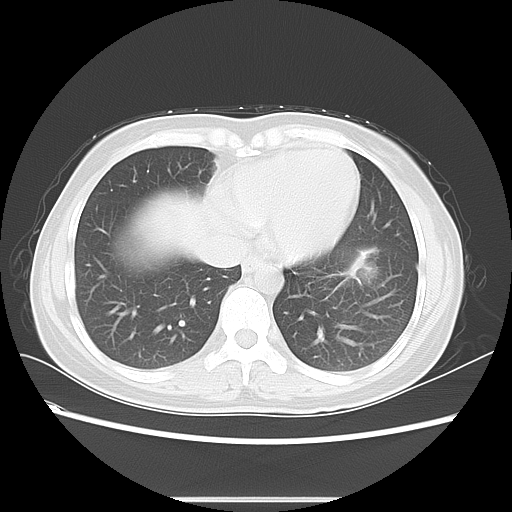
Chest CT, one axial slice; position 20 of 55 along the scan axis; reconstruction kernel LUNG; lung window (W 1500 / L -600 HU); 5 mm slice thickness; 512 × 512 image matrix, field of view 350 × 350 mm. Patient: female, 41 years. Case-level facts recorded for this patient, not image findings: clinical TNM (as recorded): T1c N3 M1b.
Outlined on this slice (bounding box drawn by a radiologist):
- lung tumour (recorded histology: adenocarcinoma): bounding box (x1, y1, x2, y2) in pixels: (345, 244, 384, 288)